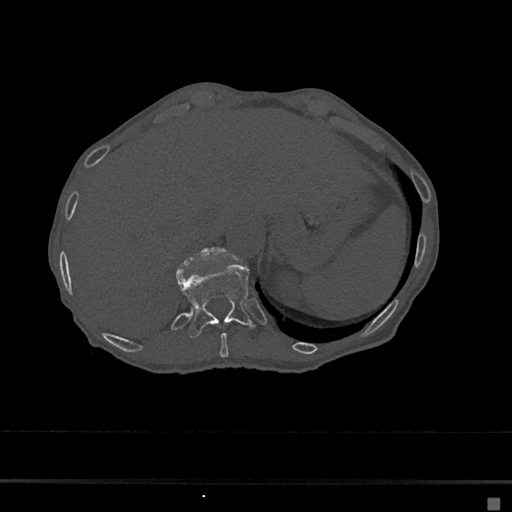
CT including the spine, one axial slice. Position 181 of 797 along the scan axis. 120 kVp. Bone window (W 1800 / L 400 HU). 0.5 mm slice thickness. 512 × 512 image matrix, field of view 360 × 360 mm. Female patient, age 68 years. Case-level facts recorded for this patient, not image findings: primary cancer: renal.
Outlined on this slice (semi-automatically segmented with operator editing):
- T10 vertebra: bounding box [x1, y1, x2, y2] px = [216, 325, 228, 358]
- T11 vertebra: [176, 263, 255, 339]
- T12 vertebra: [180, 249, 213, 267]